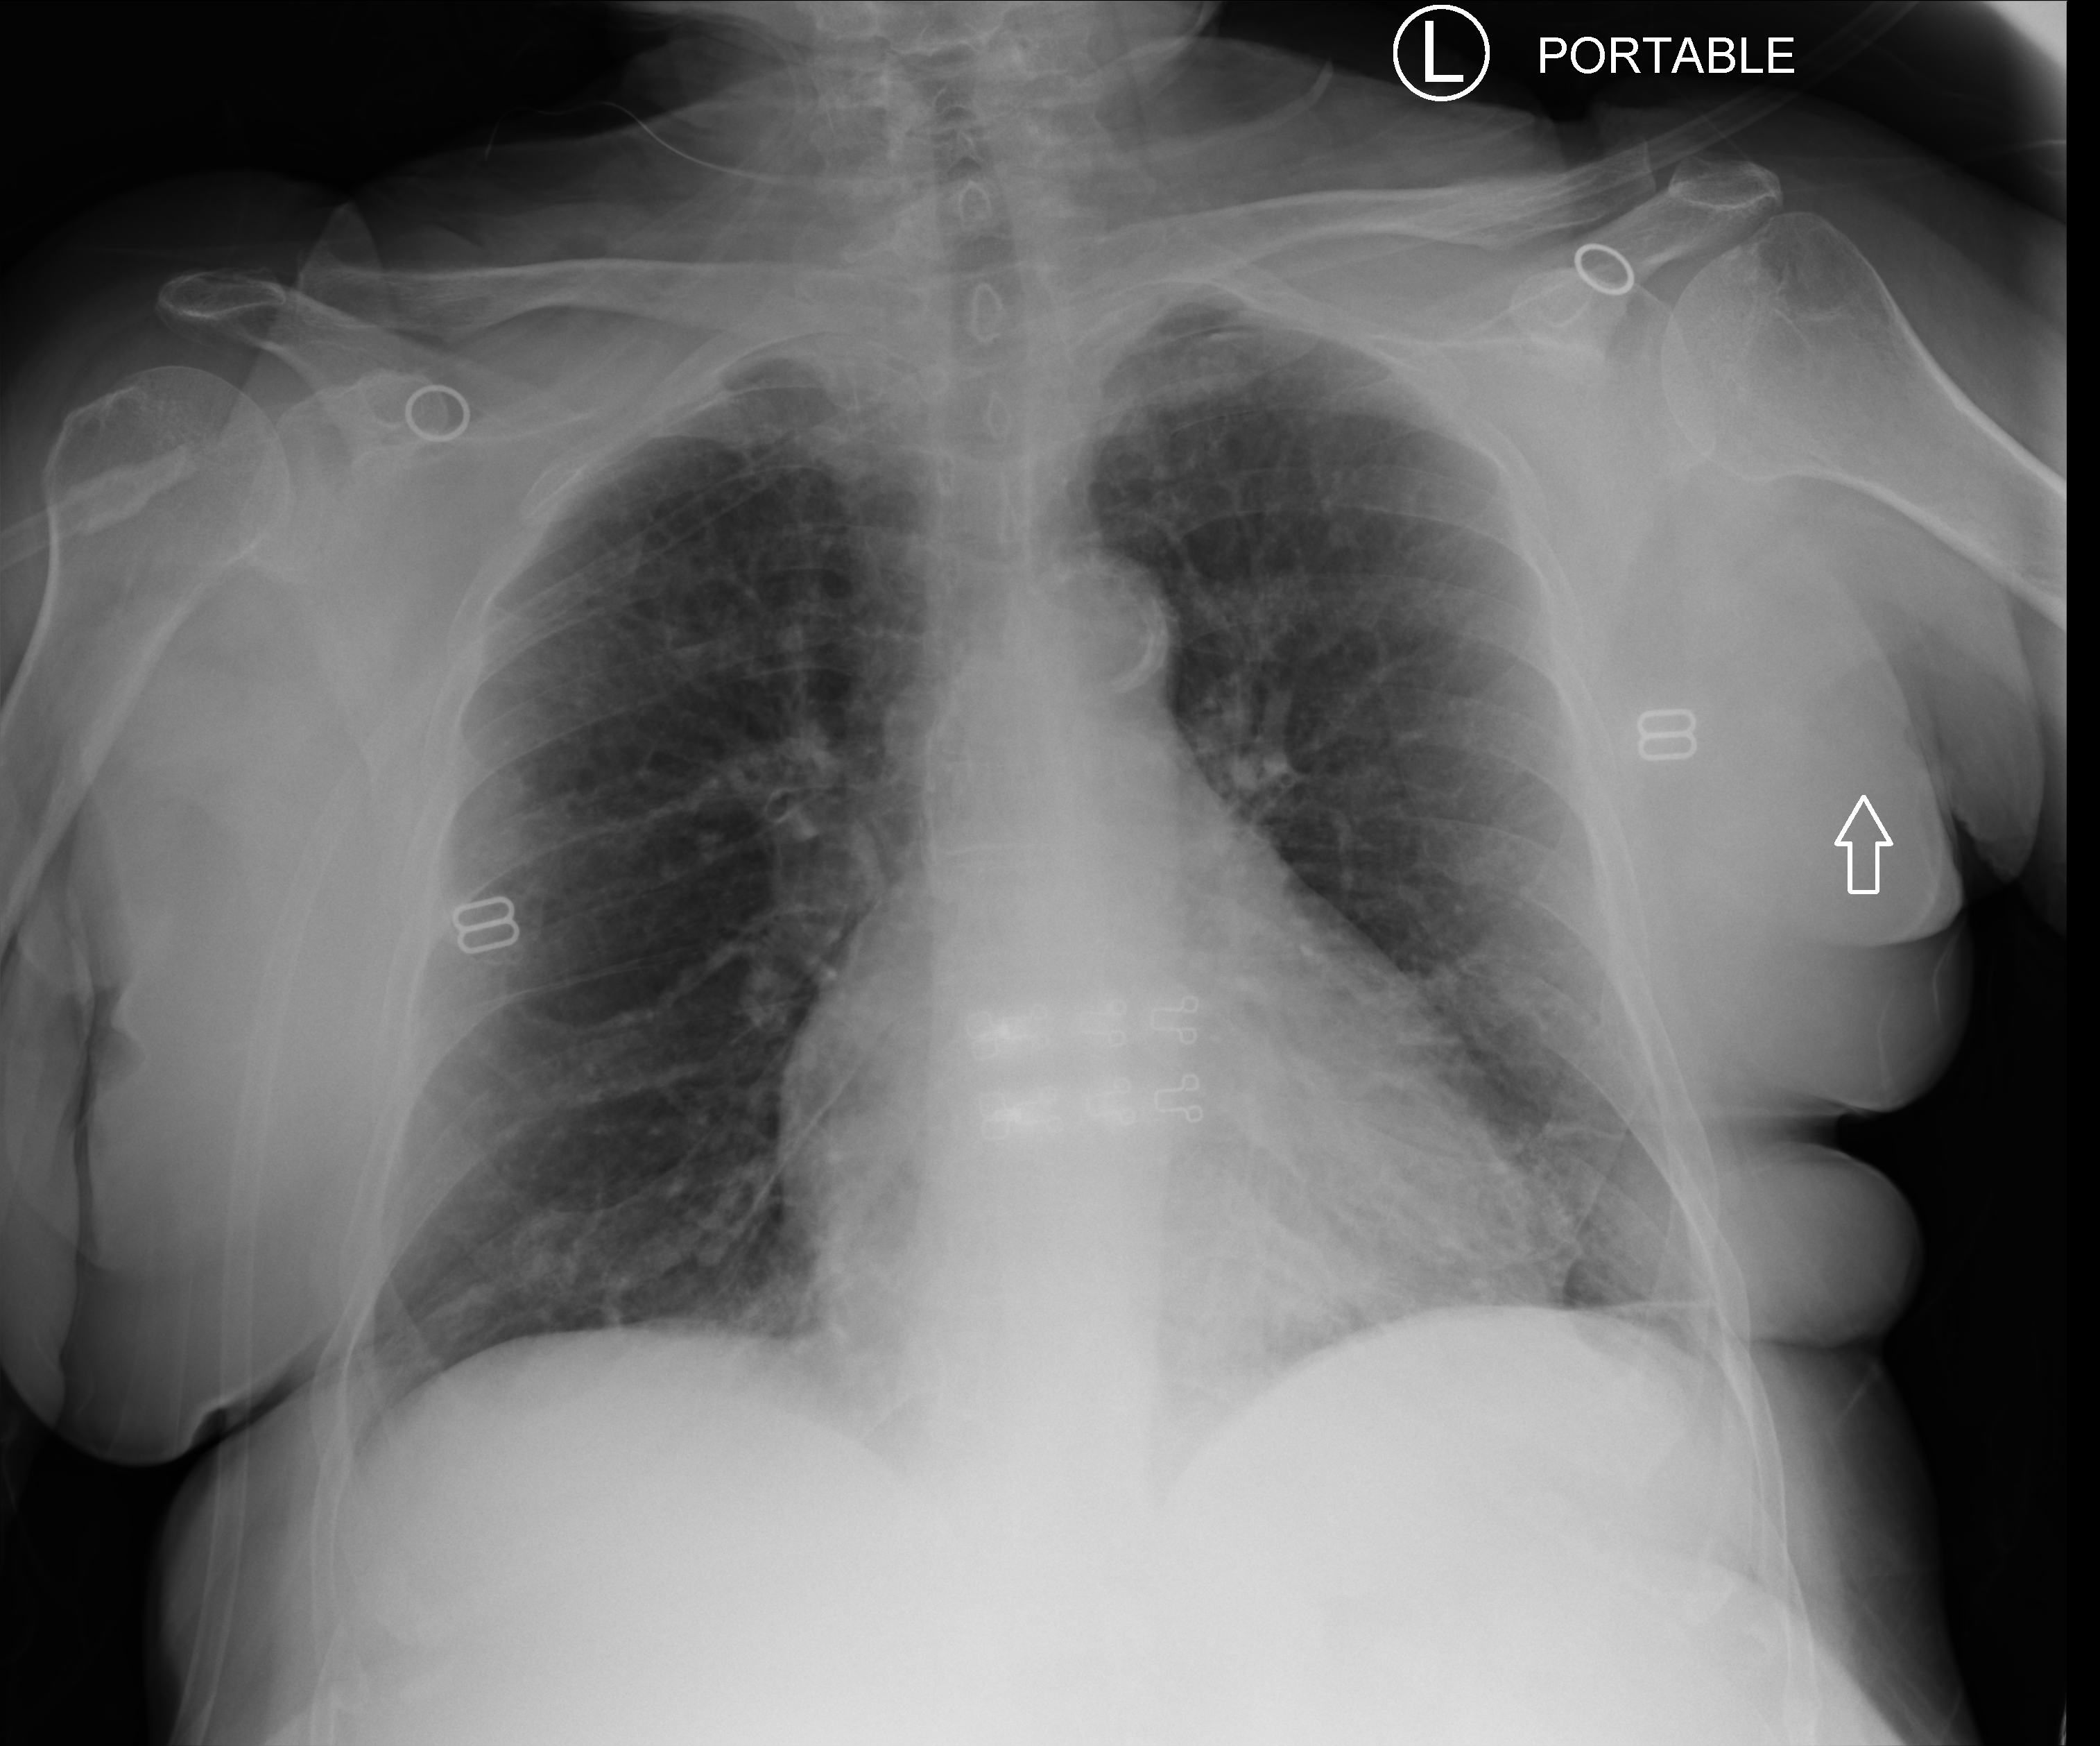
Chest X-ray (portable). Patient hospitalised with COVID-19; female, aged 75–90 years.
Admission-level facts for this patient (not findings on this image; timing relative to this image not recorded): mechanically ventilated during this hospital stay: no.